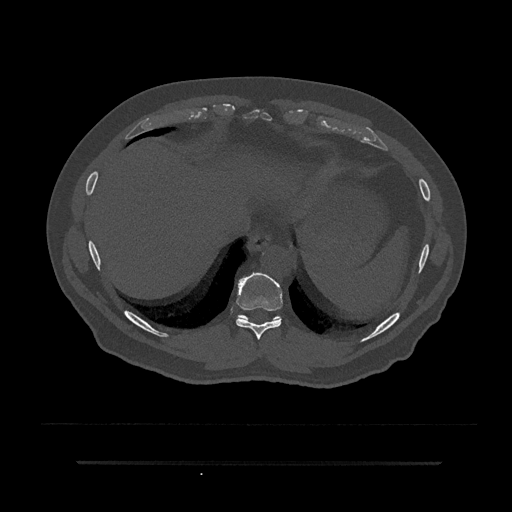
CT including the spine, one axial slice; slice 365 of 797 in the series (ordered by position); reconstruction kernel Br40s/3; 120 kVp; bone window (W 1800 / L 400 HU); 0.5 mm slice thickness; 512 × 512 image matrix. Patient: male, 59 years. Case-level facts recorded for this patient, not image findings: primary cancer: bile ducts.
Annotated regions visible in this slice (semi-automatic segmentation, software-assisted and operator-edited):
- T10 vertebra: bounding box <238,273,279,321> (left, top, right, bottom; pixels)
- T9 vertebra: <236,272,283,340>